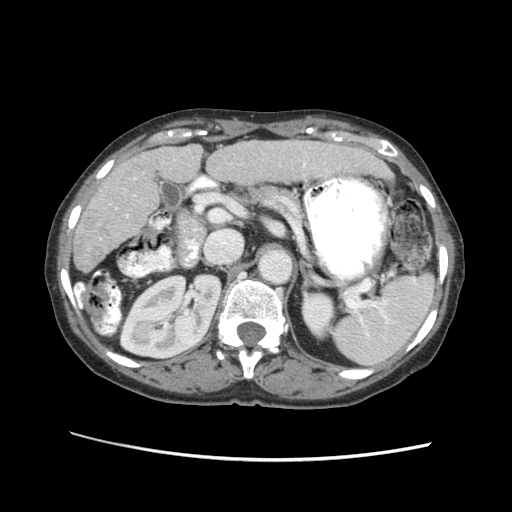
Contrast-enhanced abdominal CT (liver protocol), one axial slice. Slice 29 of 63 in the series (ordered by position). Soft-tissue window (W 400 / L 40 HU). 2.5 mm slice thickness. 512 × 512 image matrix, field of view 340 × 340 mm. Case-level facts recorded for this patient, not image findings: diagnosis: hepatocellular carcinoma (patient treated with transarterial chemoembolisation; whether this scan precedes or follows treatment is not stated here); TNM stage (as recorded): Stage-I.
Annotated regions visible in this slice (semi-automatic segmentation, software-assisted and operator-edited):
- liver parenchyma outside the tumour (the mass and vessels are separate outlines, so this box may not span the whole liver): bounding box (x1, y1, x2, y2) in pixels: (80, 134, 392, 246)
- liver vessels: (132, 155, 377, 194)